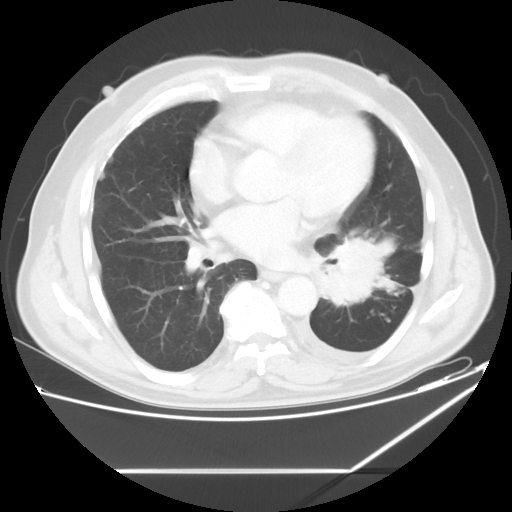
Chest CT, one axial slice. Slice 28 of 60 in the series (ordered by position). Reconstruction kernel STANDARD. 120 kVp. Lung window (W 1500 / L -600 HU). 5 mm slice thickness. 512 × 512 image matrix, field of view 395 × 395 mm. Male patient, age 62 years. From the clinical record (not read from this slice): clinical TNM (as recorded): T3 N0 M1.
Structures marked on this image (bounding box drawn by a radiologist):
- lung tumour (recorded histology: adenocarcinoma): bounding box <317,228,398,310> (left, top, right, bottom; pixels)
- lung tumour (recorded histology: adenocarcinoma): <320,231,398,312>